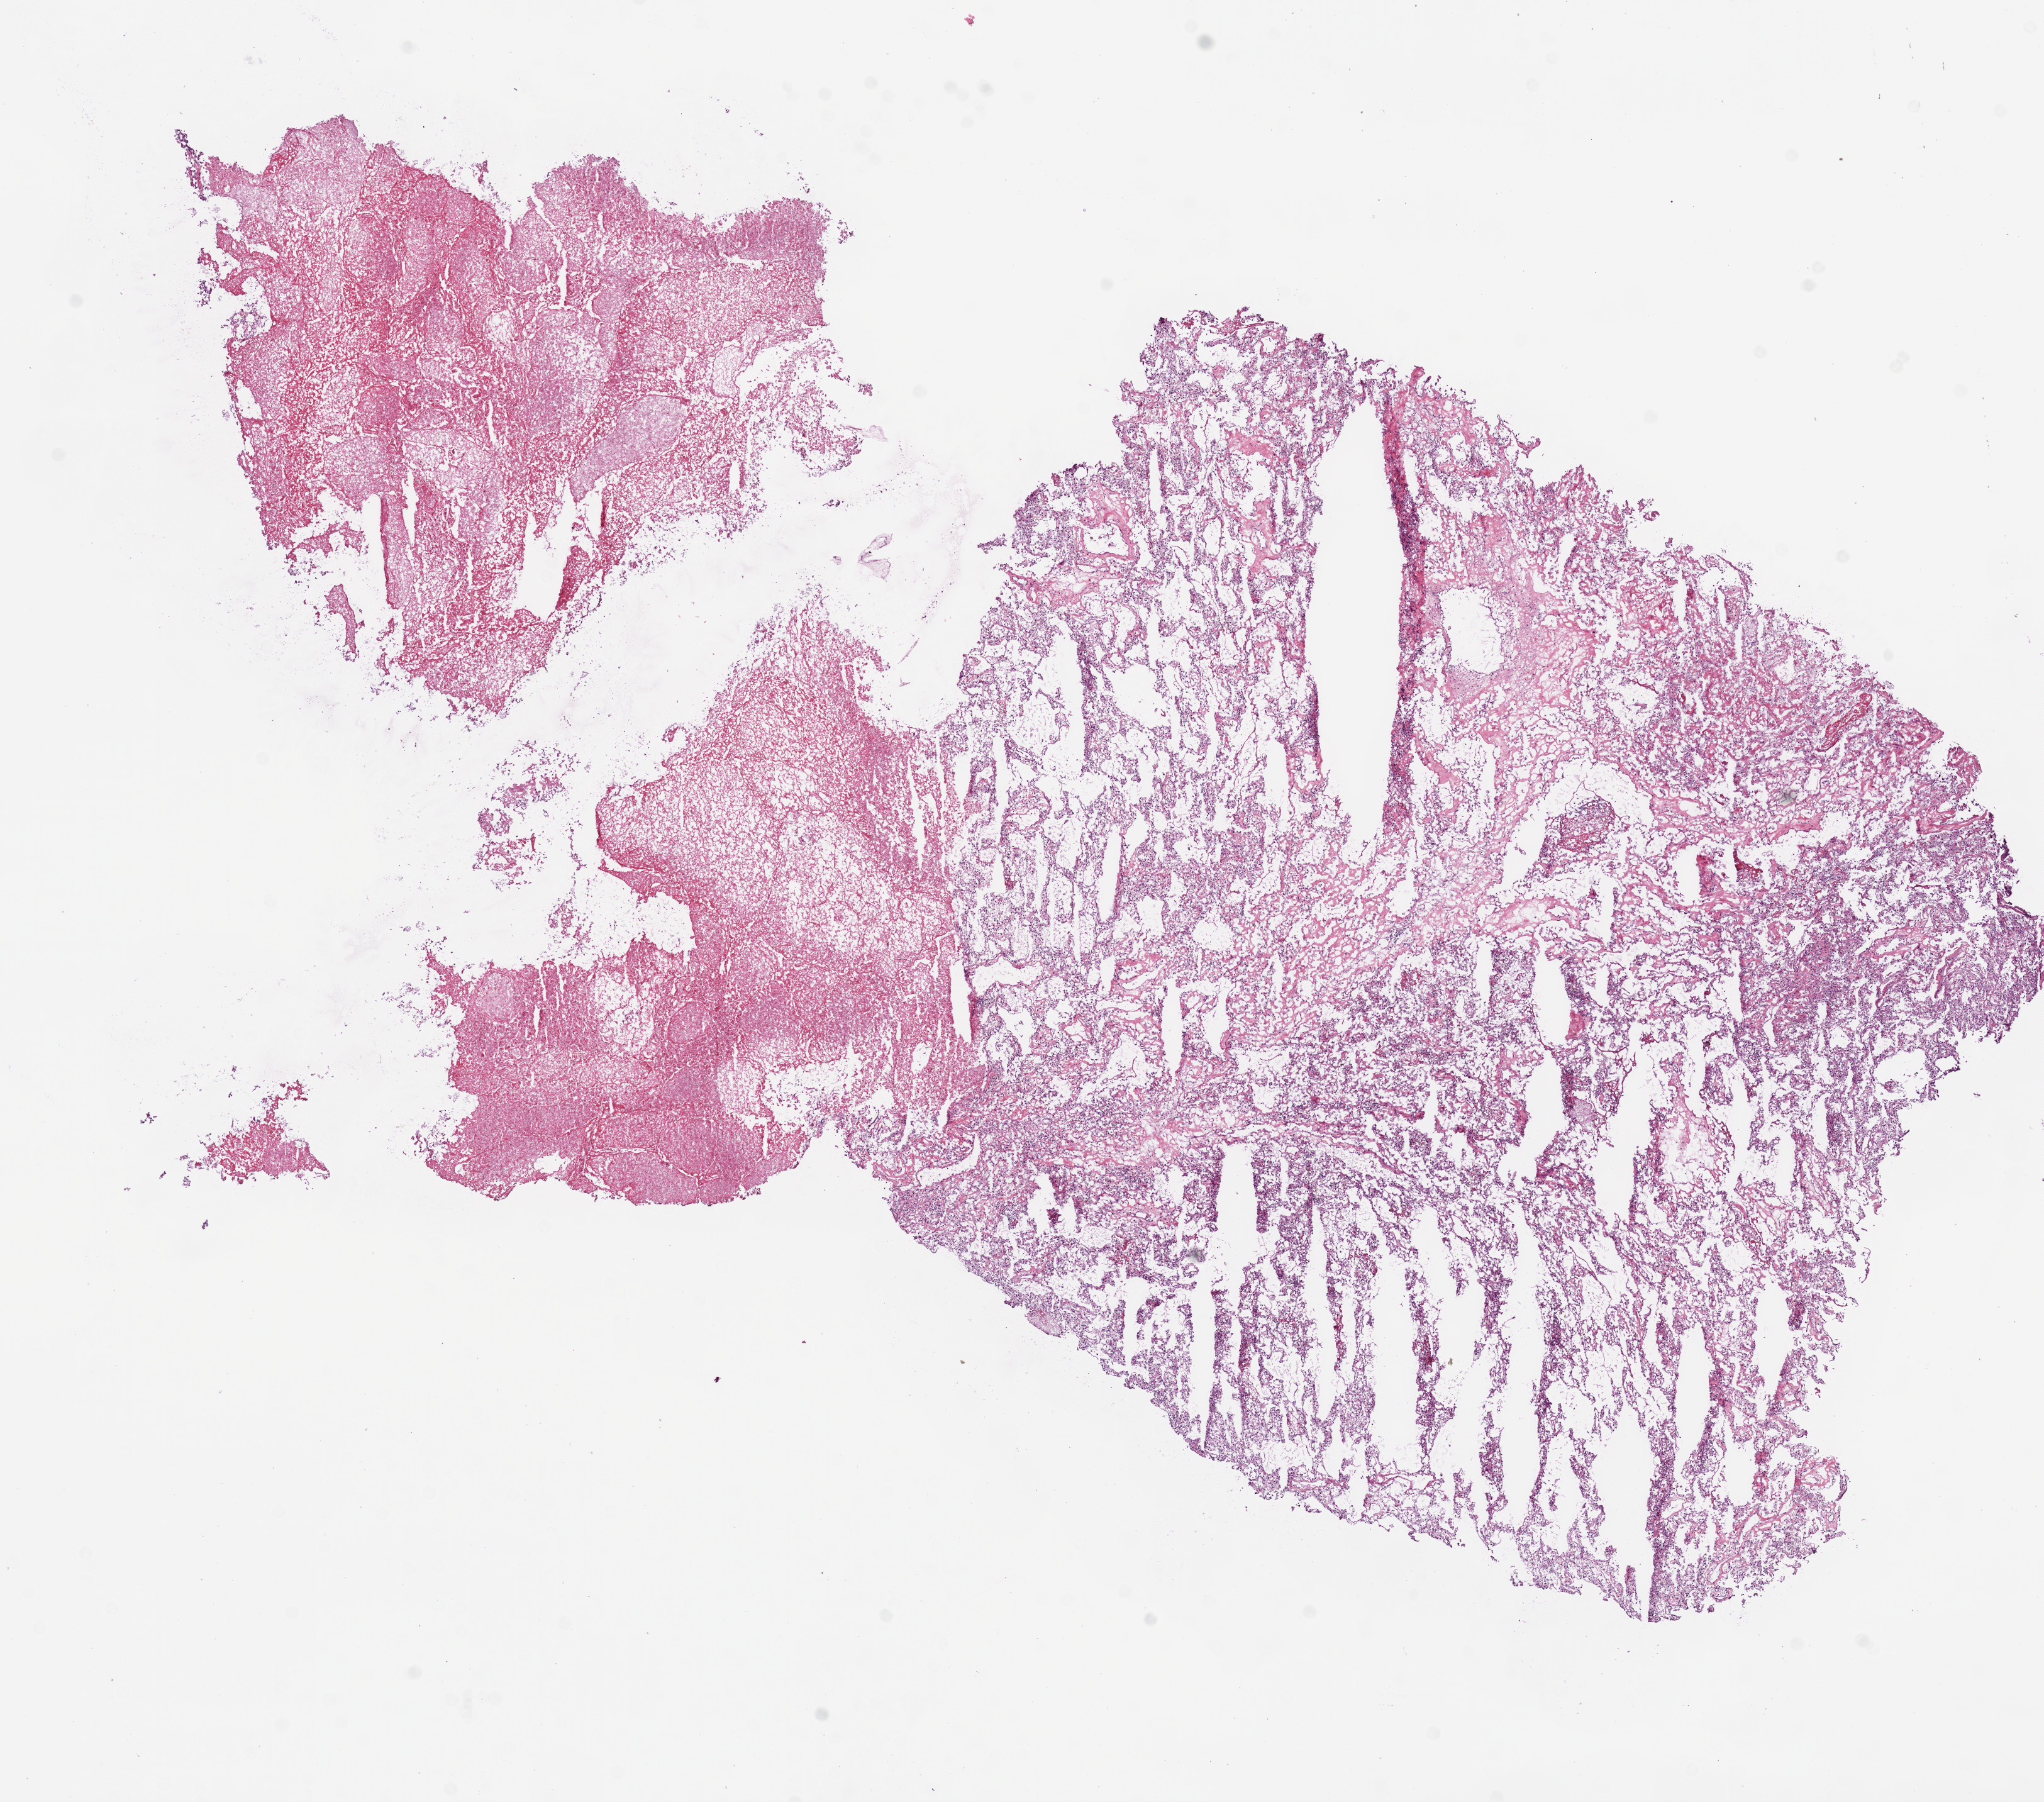
Hematoxylin and eosin (H&E) stained whole-slide image — whole scanned area (about 13.0 x 11.5 mm) shown as a low-resolution overview. Frozen section from the bottom of the tissue portion. Kidney, primary tumour sample. Patient: male, age at initial diagnosis 70 years. Histologic grade: G3 (poorly differentiated). Composition of this section per pathologist review: tumour cells 85%, tumour nuclei 90%, normal cells 0%, stromal cells 0%, necrosis 15%.
AJCC pathologic stage: III. Diagnosis: Clear cell adenocarcinoma, NOS.